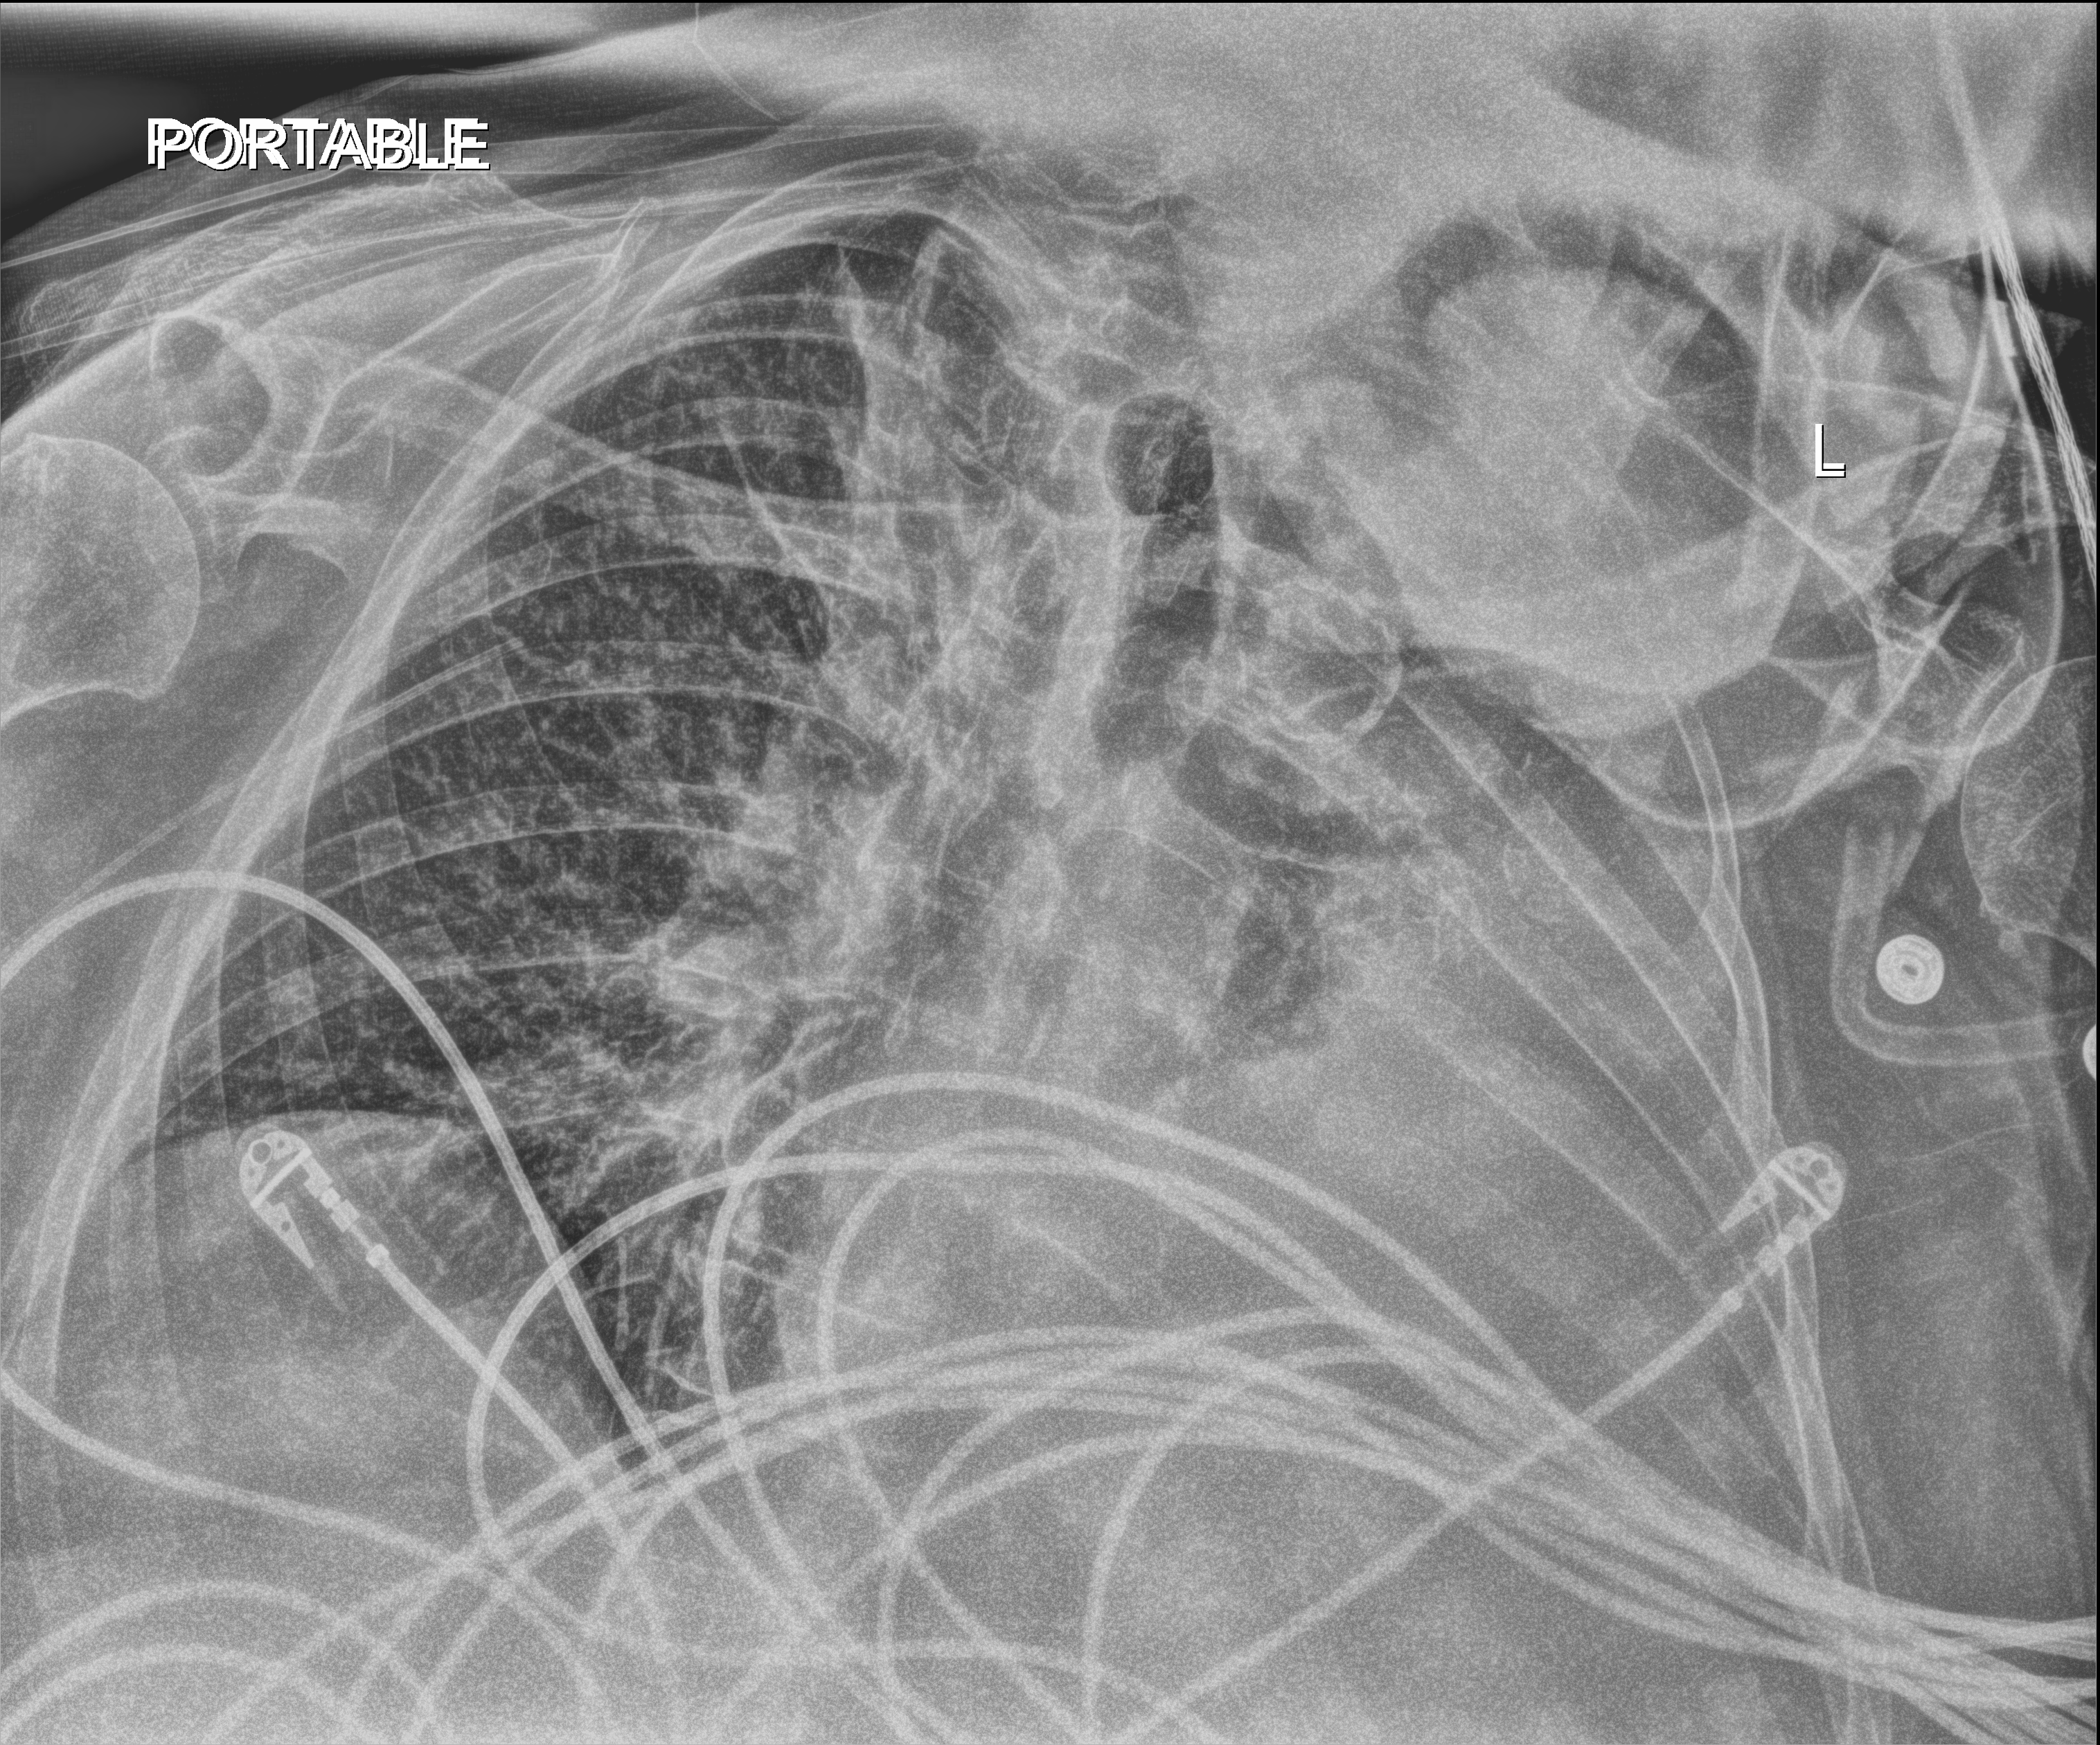
Chest X-ray (portable), anteroposterior (AP) projection. Patient hospitalised with COVID-19; female, aged 75–90 years.
From the hospital-stay record, not from the radiograph (when in the stay this image was taken is not recorded): length of hospital stay: 5 days; mechanically ventilated during this hospital stay: no.